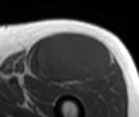
MRI of an extremity soft-tissue mass, one axial slice; slice 63 of 86 in the series (ordered by position); MR volume resampled by the dataset authors to the PET/CT grid (not the native acquisition matrix); 139 × 117 image matrix, field of view 136 × 114 mm. Male patient. From the clinical record (not read from this slice): histological type: extraskeletal osteosarcoma; grade: high; site of the primary tumour: thigh.
Structures marked on this image (expert contour drawn on MRI and transferred to this co-registered scan by the dataset authors):
- gross tumour volume (mass): bounding box [x1, y1, x2, y2] px = [36, 34, 112, 83]